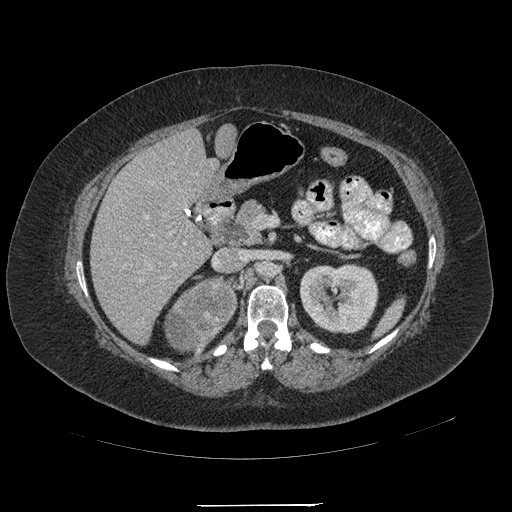
Contrast-enhanced abdominal CT, one axial slice; position 117 of 217 along the scan axis; reconstruction kernel STANDARD; soft-tissue window (W 400 / L 40 HU); 1.25 mm slice thickness; 512 × 512 image matrix. Female patient, age 55 years. From the clinical record (not read from this slice): diagnosis: adrenocortical carcinoma; tumour side: right adrenal; tumour size at pathology: 11 cm; Ki-67 index: 20 %; stage (as recorded): 2.
Annotated regions visible in this slice (semi-automatically segmented with operator editing):
- mass: box from (x=167, y=280) to (x=235, y=350) px